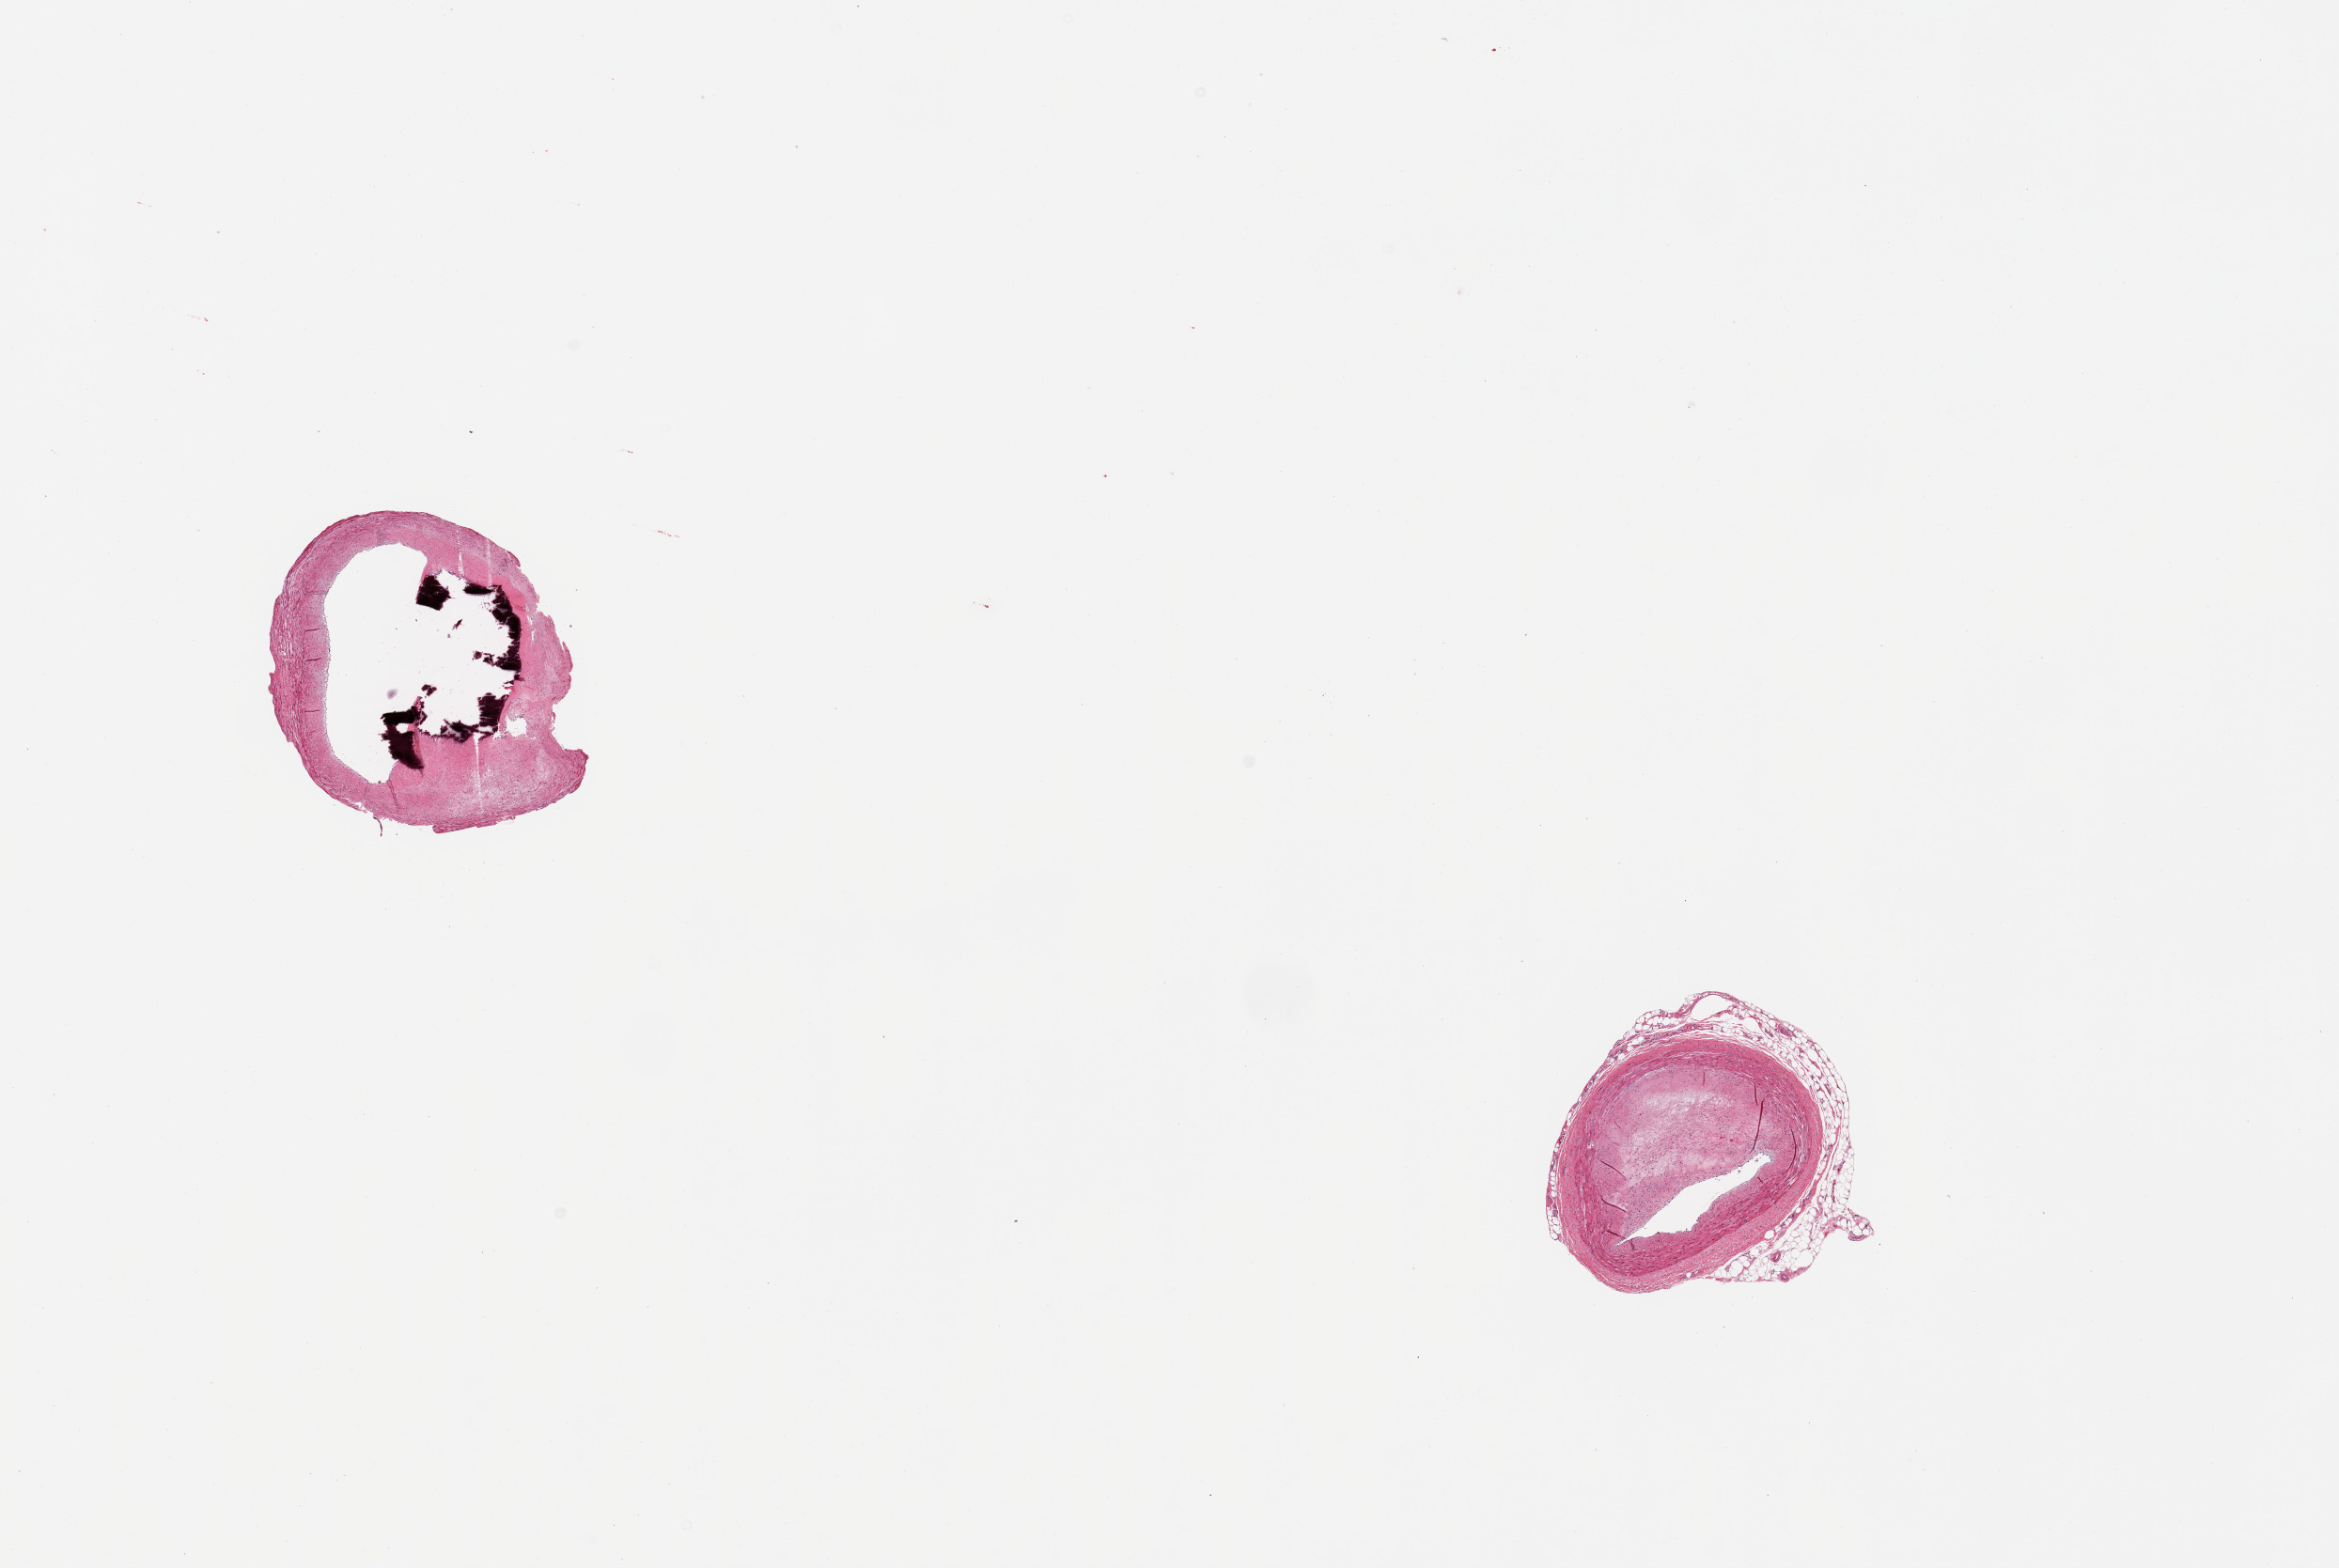
Digitized hematoxylin and eosin (H&E)-stained section — shown as a low-resolution overview of the whole scanned area (about 19.7 x 13.2 mm). PAXgene-fixed paraffin-embedded (PFPE) section. Sampled site (target tissue): coronary artery. Tissue donor sample. Female donor.
* review note (as recorded): 2 pieces, subtotally occlusive atherosis, focally calcified